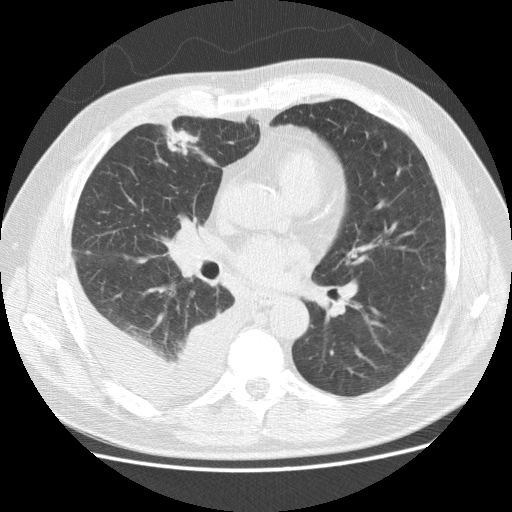
Low-dose screening chest CT, axial slice; baseline annual screen; lung window (W 1500 / L -600 HU); standard (soft-tissue) reconstruction kernel (STANDARD); slice 78 of 142 in the series; 512 × 512 image matrix. Male, age 65 years at enrolment. Current smoker at enrolment.
Expert-annotated lung lesion, box from (x=149, y=121) to (x=216, y=172) px. The exam's reader record, not a measurement of the box and not confirmed to be the same lesion: non-calcified nodule or mass ≥4 mm, right middle lobe, 22 × 15 mm, spiculated (stellate) margins, mixed attenuation. Official screen result: positive, change unspecified: nodule(s) >= 4 mm or enlarging nodule(s), mass(es), or other non-specific abnormalities suspicious for lung cancer.